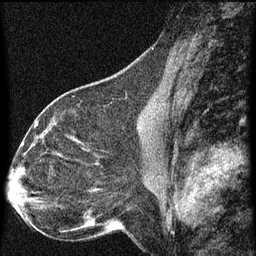
Breast MRI (dynamic contrast-enhanced), one sagittal slice; slice 37 of 60 in the series (ordered by position); dynamic contrast-enhanced series, image 2 of 3 at this slice position (ordered by acquisition); 1.5 T; TE 4.2 ms, TR 8 ms; 2 mm slice thickness; 256 × 256 image matrix. Patient: female, 44 years.
Outlined on this slice (semi-automatic segmentation, software-assisted and operator-edited):
- analysis volume of interest (the breast-tissue region the enhancement analysis was run in; not a lesion): bounding box [x1, y1, x2, y2] px = [49, 128, 95, 169]
- tumour enhancement mask (voxels above the 70 % enhancement threshold inside the analysis volume of interest): [55, 140, 79, 161]